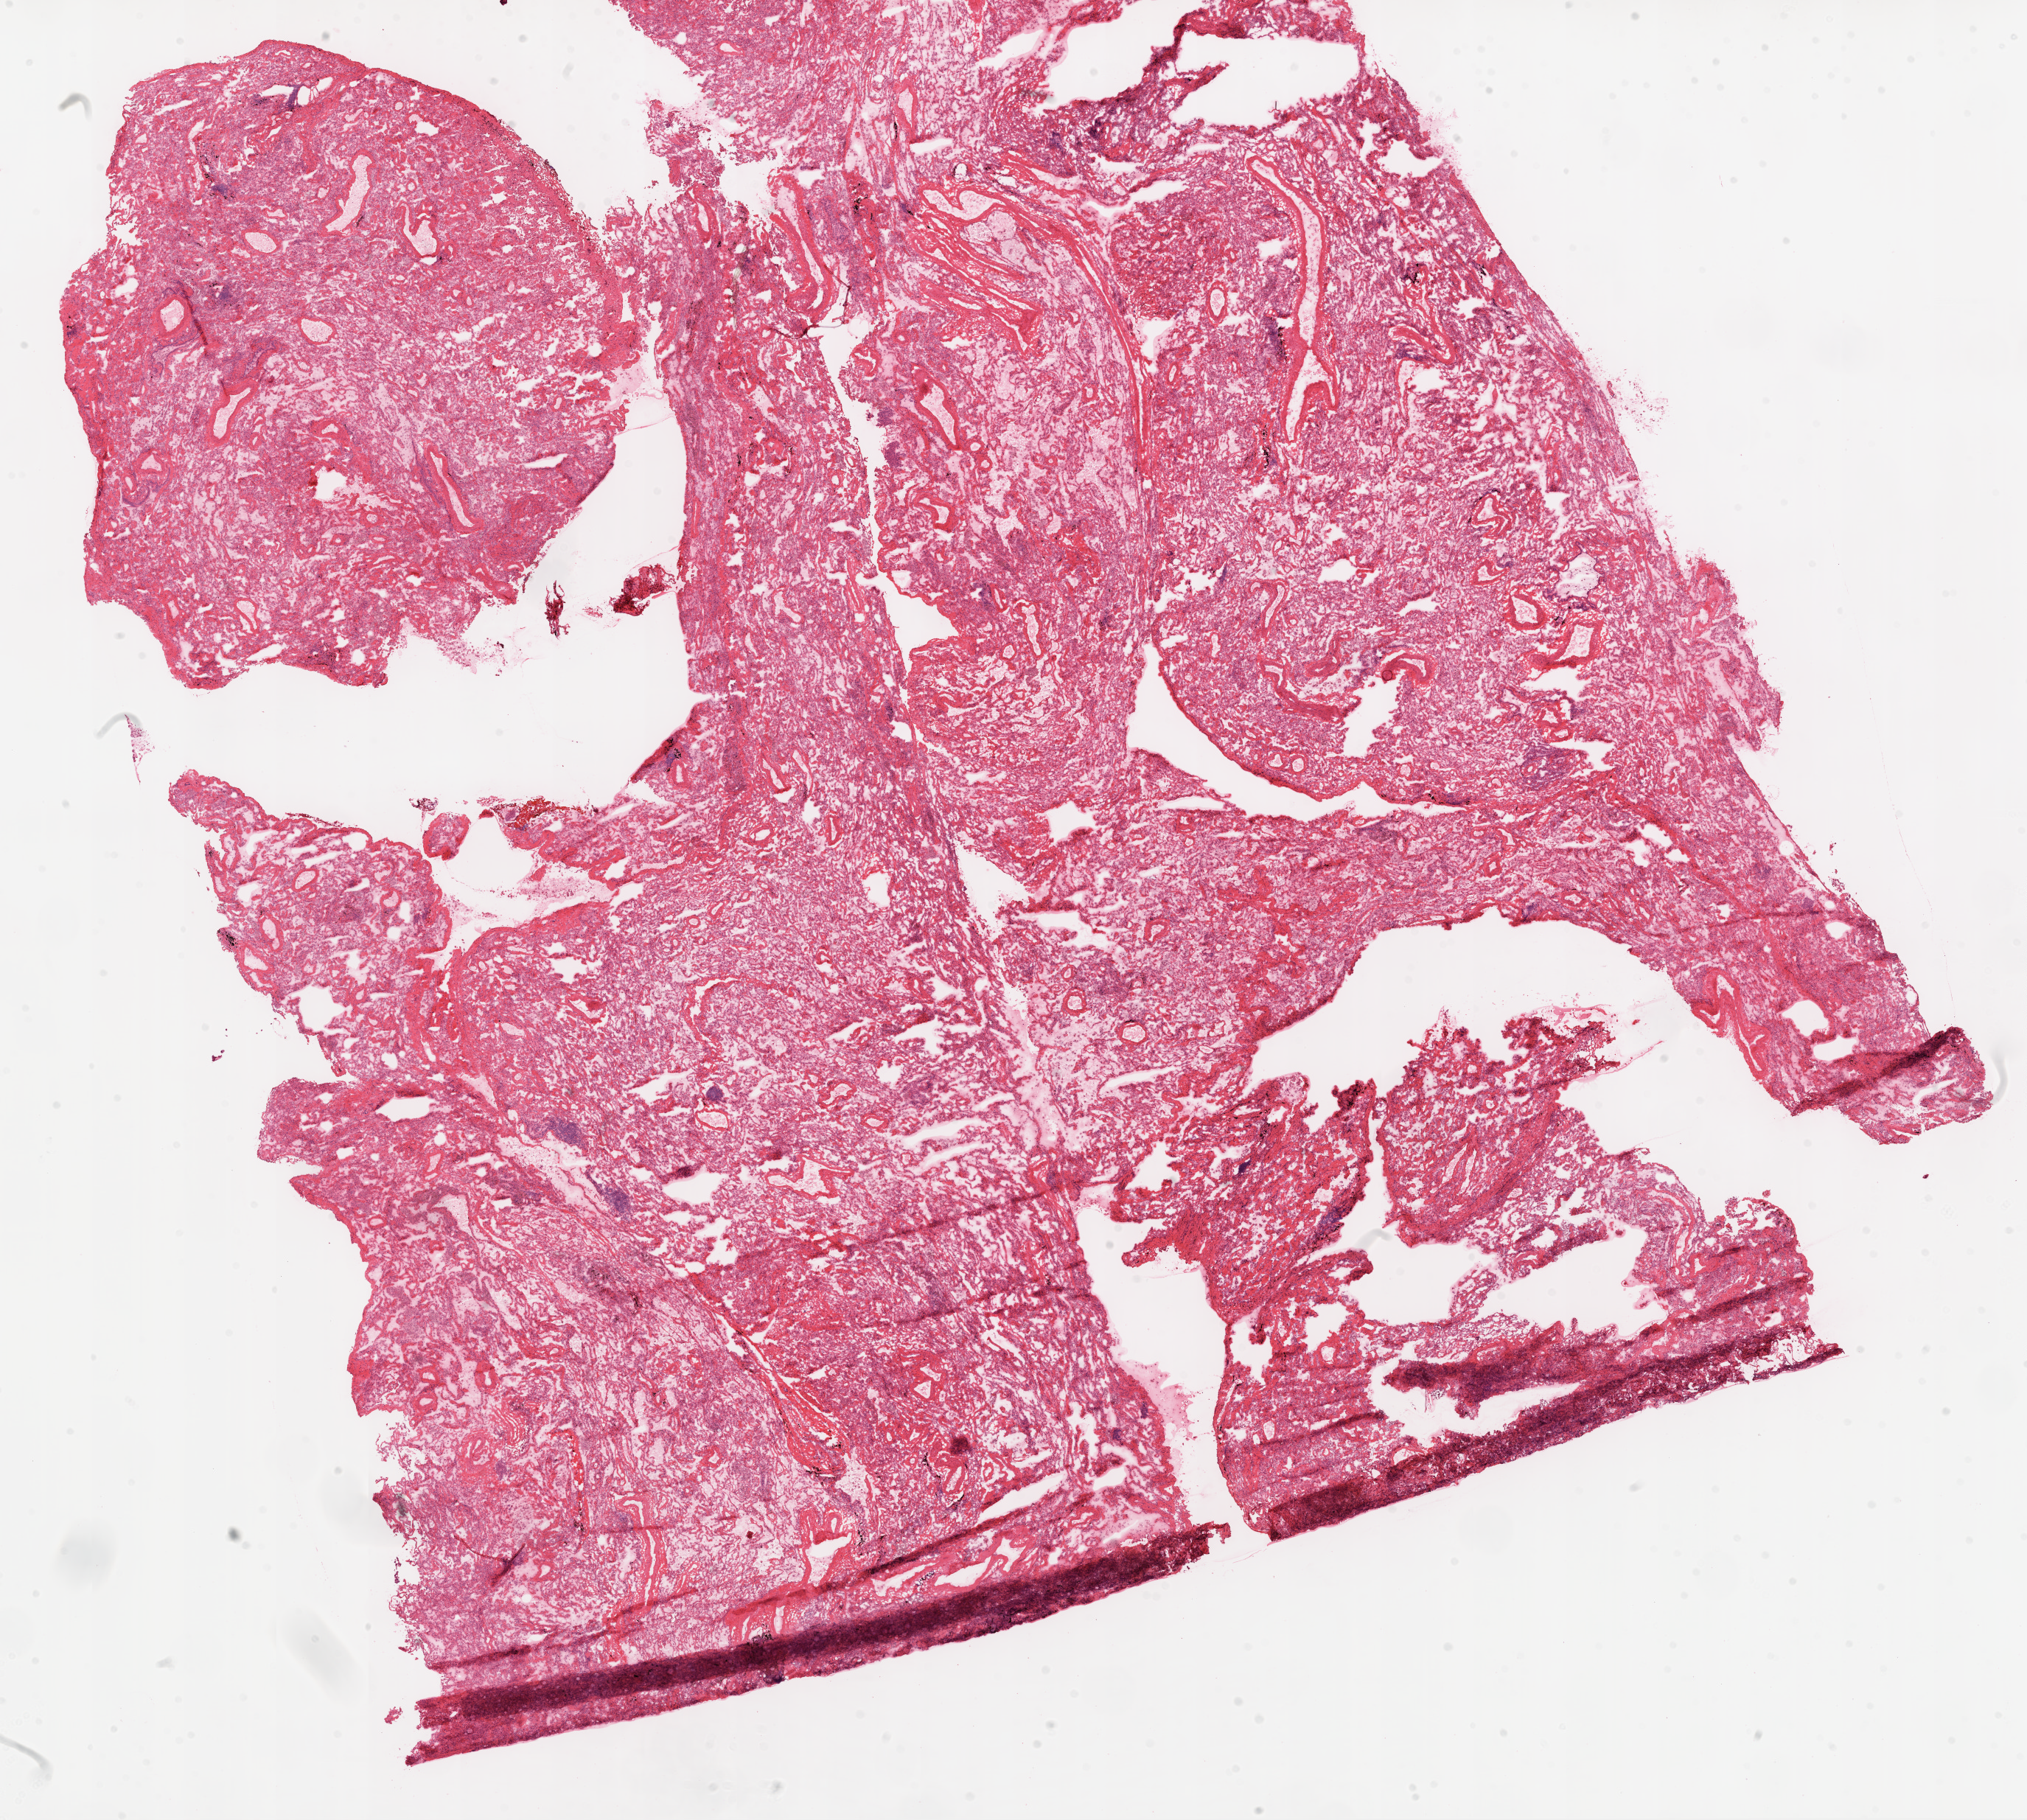
Digitized H&E-stained tissue section (whole slide) — a low-resolution overview of the entire scanned area, about 22.1 x 19.8 mm (from a 20x scan). Frozen section from the top of the tissue portion. Lung, solid tissue normal (non-tumour tissue) sample. Female, age 73 years at initial diagnosis.
This section: solid tissue normal (non-tumour) sample from the same patient. Patient diagnosis: Squamous cell carcinoma, NOS (upper lobe, lung).